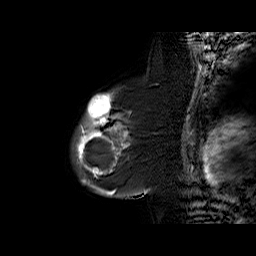
Breast MRI (dynamic contrast-enhanced), one sagittal slice. Slice 47 of 60 in the series (ordered by position). Dynamic contrast-enhanced series, time point 2 of 6 at this slice position (early post-contrast). 1.5 T. TE 6.3 ms, TR 32.4 ms. 4 mm slice thickness. 256 × 256 image matrix, field of view 200 × 200 mm. Female patient. Case-level facts recorded for this patient, not image findings: setting: breast cancer imaged before/during neoadjuvant chemotherapy; receptor status: triple-negative.
Structures marked on this image (semi-automatically segmented with operator editing):
- analysis volume of interest (the breast-tissue region the enhancement analysis was run in; not a lesion): box from (x=71, y=89) to (x=133, y=187) px
- tumour enhancement mask (voxels above the 100 % enhancement threshold inside the analysis volume of interest): (x=76, y=93)–(x=128, y=187)